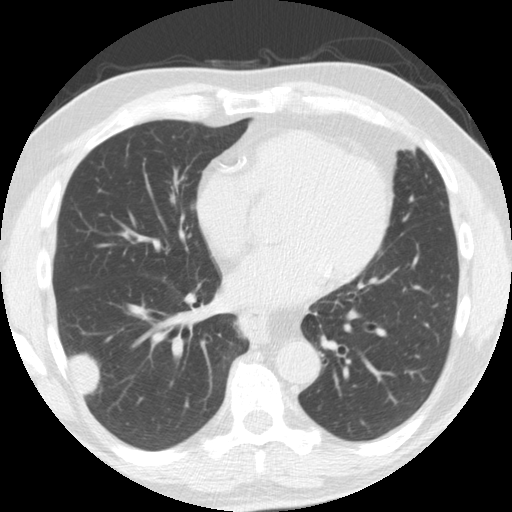
Chest CT (low-dose screening protocol), one axial image. Second annual screen. Lung window (W 1500 / L -600 HU). 2.5 mm slice thickness. Standard (soft-tissue) reconstruction kernel (STANDARD). 120 kVp. Slice 101 of 174 in the series. 512 × 512 image matrix. Male, age 61 years at enrolment. Former smoker at enrolment.
• Expert-annotated lung lesion, bounding box (x1, y1, x2, y2) in pixels: (46, 323, 114, 399).
• The exam's reader record, not a measurement of the box and not confirmed to be the same lesion: non-calcified nodule or mass ≥4 mm, right lower lobe, 33 × 19 mm, smooth margins, soft tissue attenuation, pre-existing on the prior screen: yes; interval growth: yes.
• Official screen result: positive, change unspecified: nodule(s) >= 4 mm or enlarging nodule(s), mass(es), or other non-specific abnormalities suspicious for lung cancer.
• Lung cancer was diagnosed 30 days after this screen: adenosquamous carcinoma, right lower lobe, poorly differentiated (G3), stage IV (AJCC 6th edition), 45 mm at pathology.